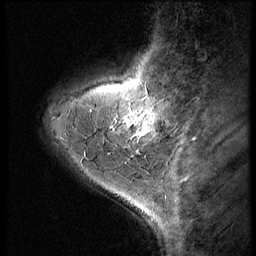
Breast MRI (dynamic contrast-enhanced), one sagittal slice. Position 14 of 56 along the scan axis. Dynamic contrast-enhanced series, image 2 of 3 at this slice position (ordered by acquisition). 1.5 T. TE 4.2 ms, TR 9 ms. 2.5 mm slice thickness. 256 × 256 image matrix, field of view 180 × 180 mm. Patient: female, 38 years. Case-level facts recorded for this patient, not image findings: setting: breast cancer imaged before/during neoadjuvant chemotherapy; receptor status: triple-negative.
Outlined on this slice (semi-automatically segmented with operator editing):
- analysis volume of interest (the breast-tissue region the enhancement analysis was run in; not a lesion): bounding box <107,95,179,149> (left, top, right, bottom; pixels)
- tumour enhancement mask (voxels above the 140 % enhancement threshold inside the analysis volume of interest): <124,111,158,136>